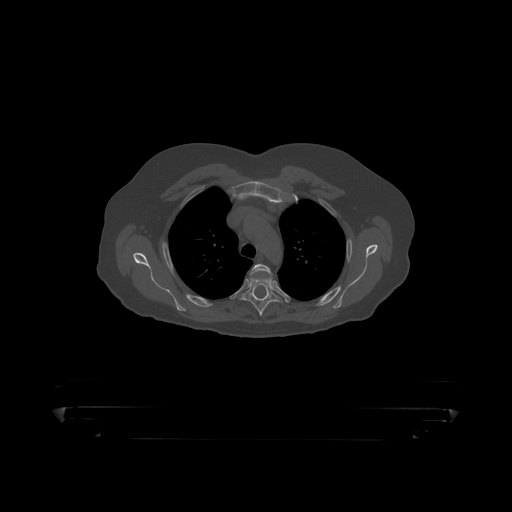
CT including the spine, one axial slice; position 342 of 390 along the scan axis; reconstruction kernel STANDARD; bone window (W 1800 / L 400 HU); 512 × 512 image matrix. Patient: male, 60 years. Case-level facts recorded for this patient, not image findings: primary cancer: prostate.
Structures marked on this image (semi-automatic segmentation, software-assisted and operator-edited):
- T3 vertebra: bounding box (x1, y1, x2, y2) in pixels: (251, 264, 272, 275)
- T4 vertebra: (239, 277, 283, 317)